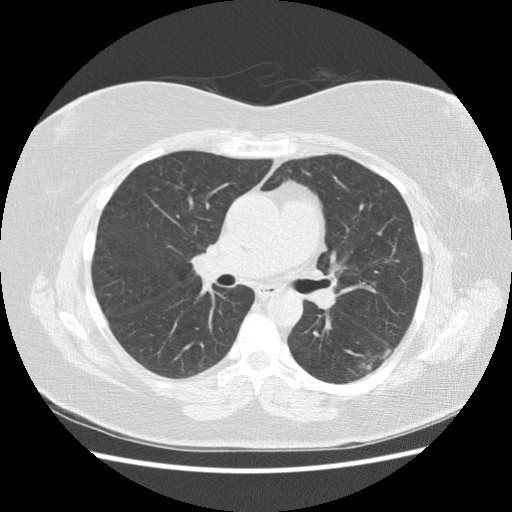
Low-dose screening chest CT, one axial slice; position 89 of 151 along the scan axis; reconstruction kernel STANDARD; lung window (W 1500 / L -600 HU); 2.5 mm slice thickness; 512 × 512 image matrix.
Outlined on this slice (outlined manually by an expert reader):
- lesion 1 (tumor, lower lobe of left lung): bounding box <357,361,373,370> (left, top, right, bottom; pixels)